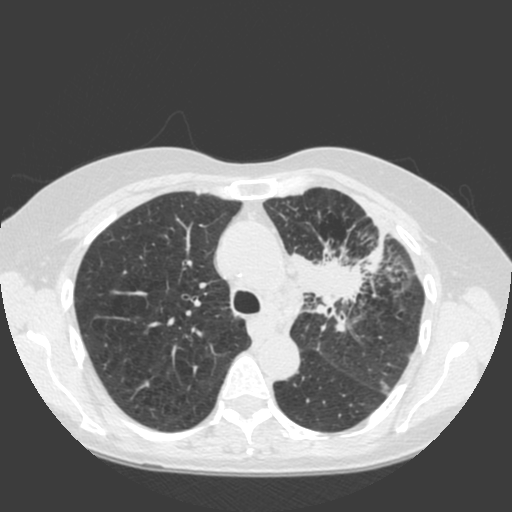
Low-dose screening chest CT, one axial slice; position 133 of 184 along the scan axis; 120 kVp; lung window (W 1500 / L -600 HU); 2 mm slice thickness; 512 × 512 image matrix.
Annotated regions visible in this slice (manually delineated by an expert):
- lesion 1 (tumor, hilum of left lung): bounding box (x1, y1, x2, y2) in pixels: (287, 224, 387, 318)